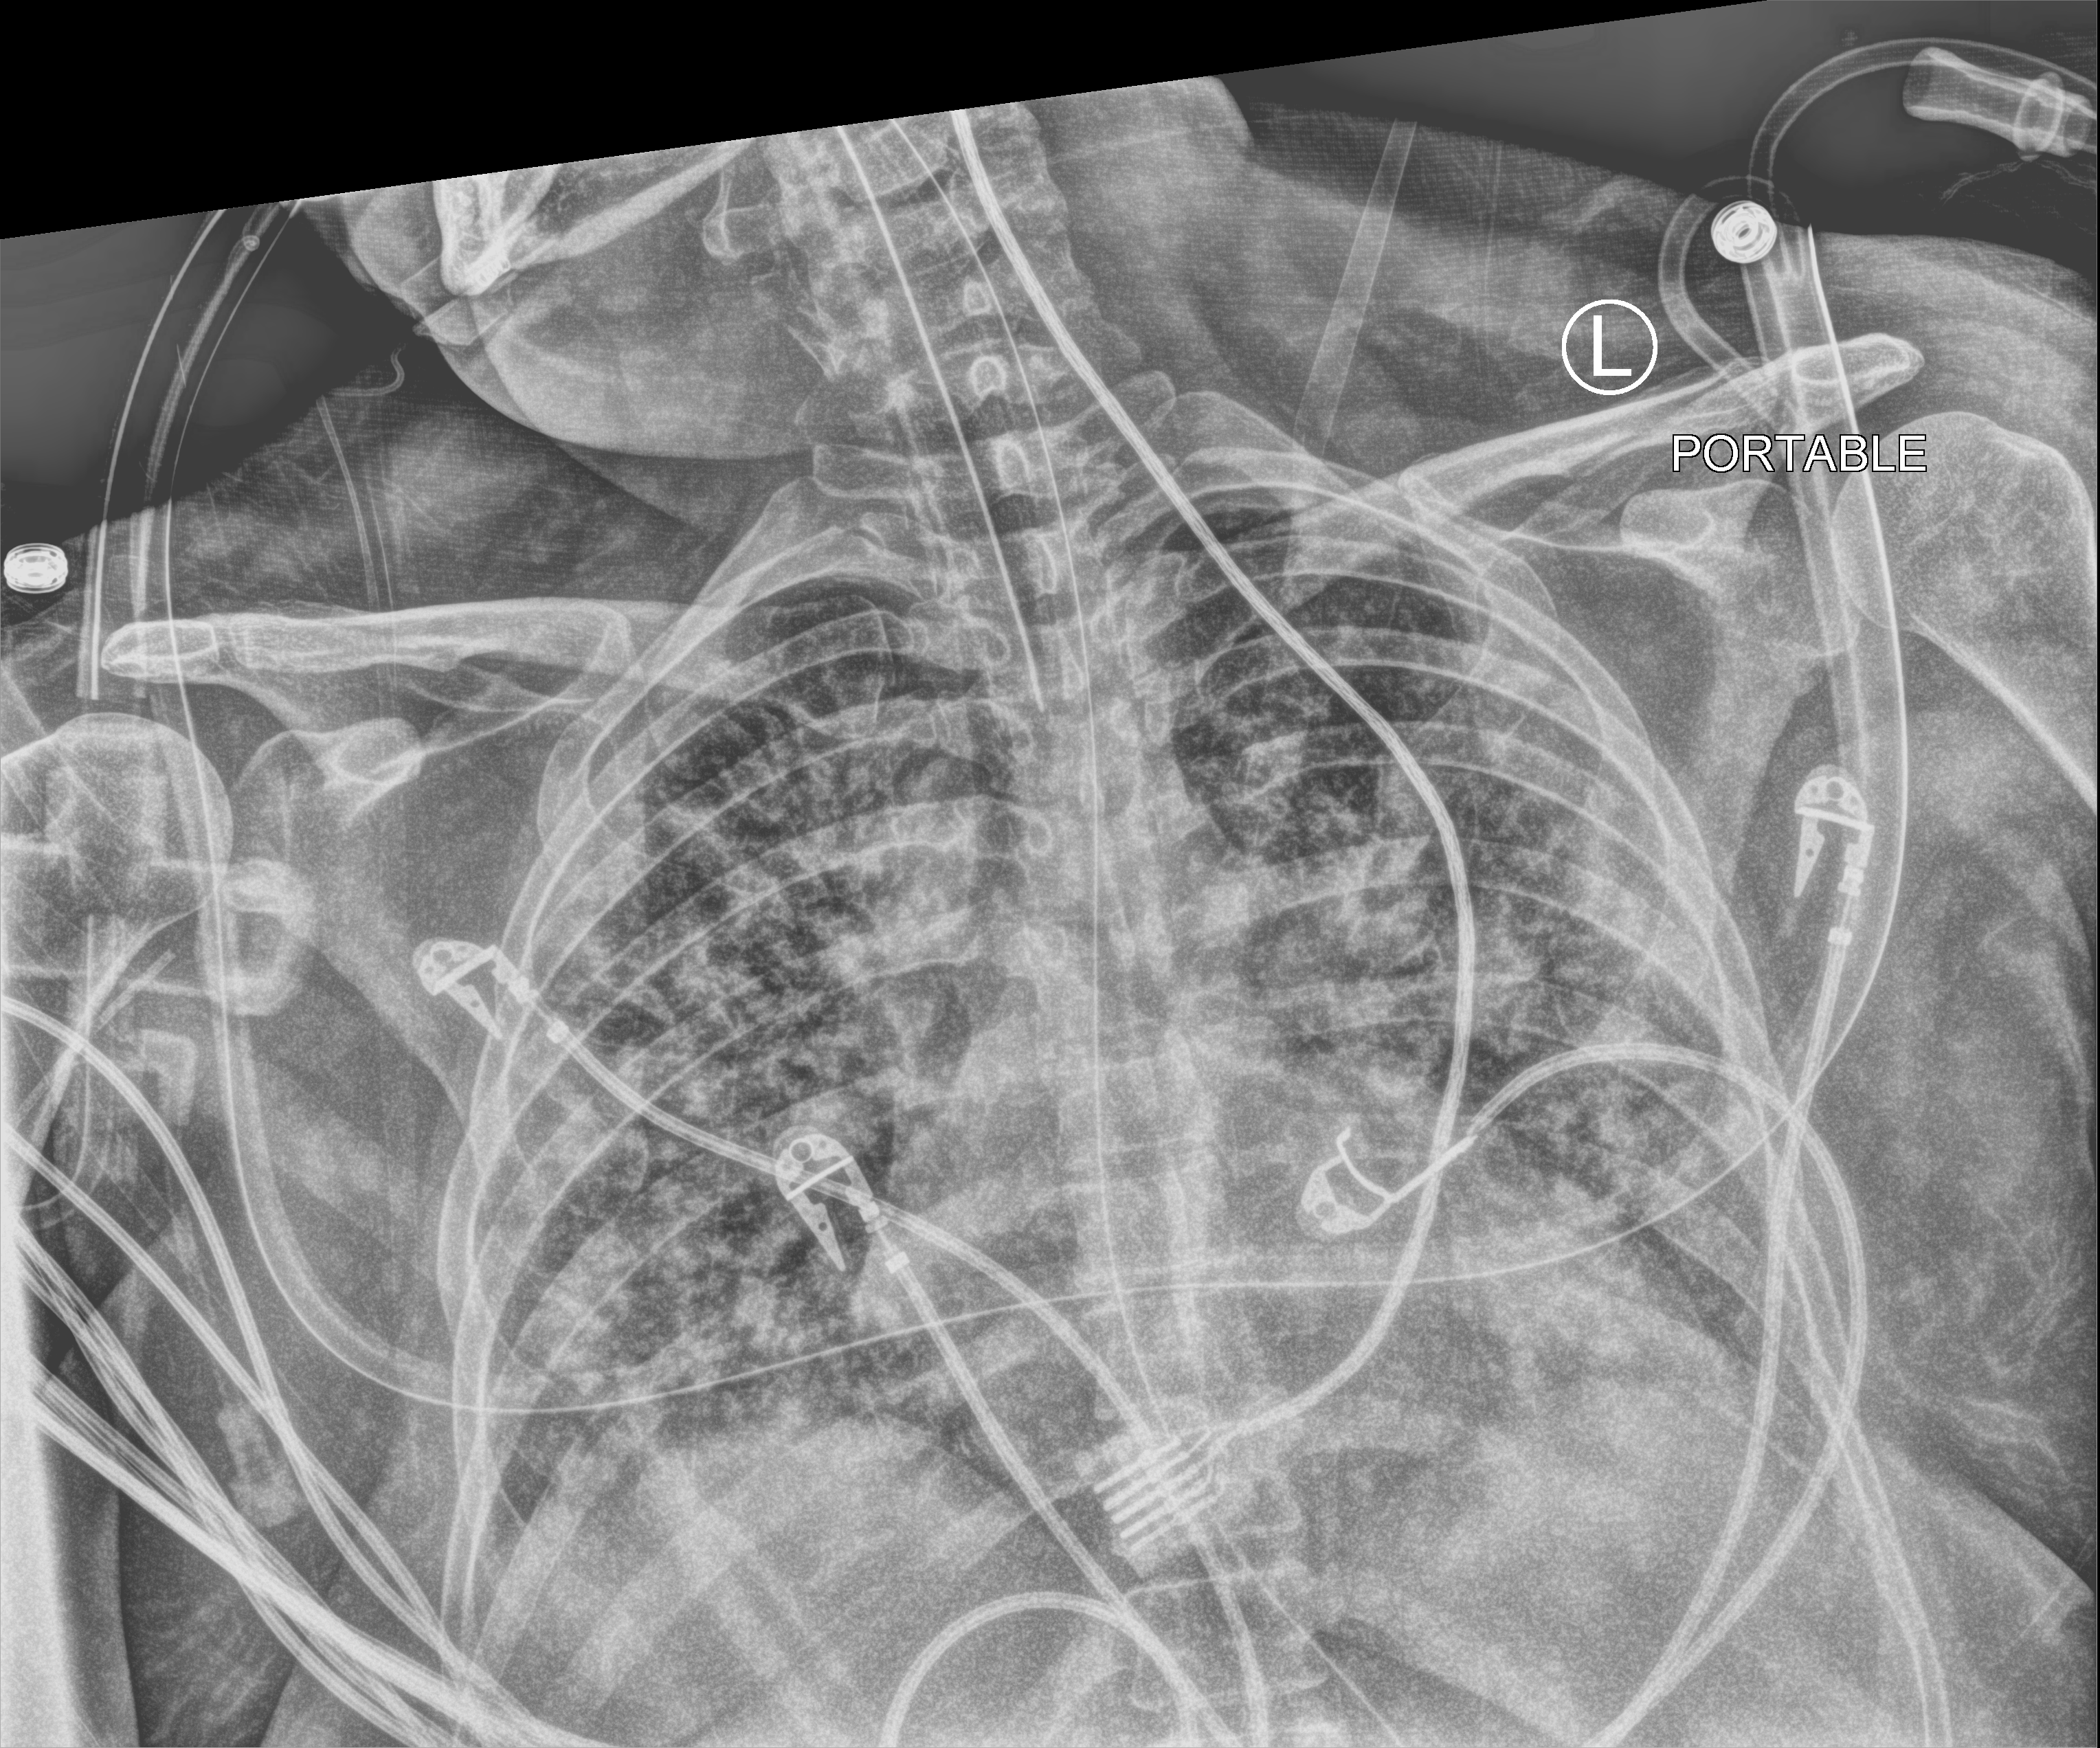
Portable chest radiograph, anteroposterior (AP) projection. Female patient hospitalised with COVID-19, age 18–59 years.
Admission-level facts for this patient (not findings on this image; timing relative to this image not recorded):
- hypertension (admission record): yes
- admitted to intensive care during this hospital stay: yes
- length of hospital stay: 31 days